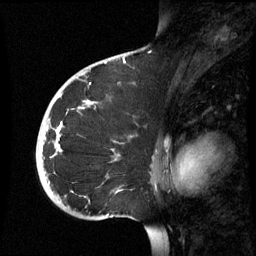
Breast MRI (dynamic contrast-enhanced), one sagittal slice; slice 39 of 60 in the series (ordered by position); dynamic contrast-enhanced series, image 2 of 3 at this slice position (ordered by acquisition); 1.5 T; TE 4.2 ms, TR 8.9 ms; 256 × 256 image matrix, field of view 220 × 220 mm. Female patient, age 35 years. Case-level facts recorded for this patient, not image findings: setting: breast cancer imaged before/during neoadjuvant chemotherapy; receptor status: HR-positive, HER2-negative.
Outlined on this slice (semi-automatic segmentation, software-assisted and operator-edited):
- analysis volume of interest (the breast-tissue region the enhancement analysis was run in; not a lesion): bounding box (x1, y1, x2, y2) in pixels: (36, 74, 156, 221)
- tumour enhancement mask (voxels above the 70 % enhancement threshold inside the analysis volume of interest): (55, 102, 91, 153)